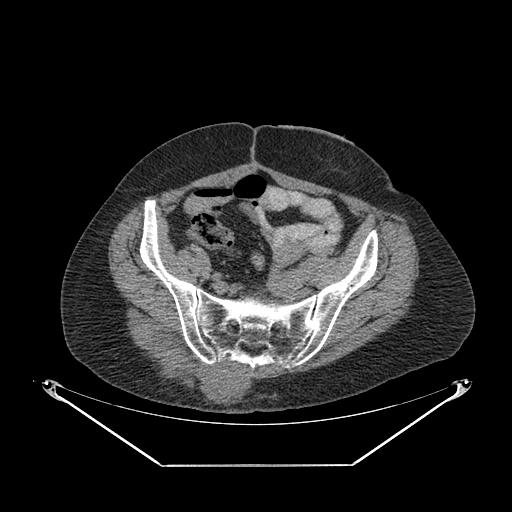
CT of an extremity soft-tissue mass (from a PET/CT study), one axial slice. Slice 73 of 267 in the series (ordered by position). Reconstruction kernel SOFT. 140 kVp. Soft-tissue window (W 400 / L 40 HU). 3.75 mm slice thickness. 512 × 512 image matrix, field of view 500 × 500 mm. Female patient. From the clinical record (not read from this slice): histological type: spindle cell suggestive of myxofibrosarcoma; grade: intermediate; site of the primary tumour: right buttock.
Outlined on this slice (expert contour drawn on MRI and transferred to this co-registered scan by the dataset authors):
- gross tumour volume (mass): bounding box (x1, y1, x2, y2) in pixels: (146, 358, 250, 407)